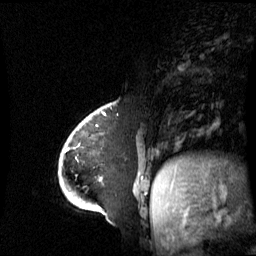
Breast MRI (dynamic contrast-enhanced), one sagittal slice; slice 17 of 60 in the series (ordered by position); dynamic contrast-enhanced series, image 2 of 3 at this slice position (ordered by acquisition); 1.5 T; TE 4.2 ms, TR 8.4 ms; 256 × 256 image matrix, field of view 270 × 270 mm. Female patient, age 43 years. Case-level facts recorded for this patient, not image findings: setting: breast cancer imaged before/during neoadjuvant chemotherapy; receptor status: triple-negative.
Annotated regions visible in this slice (semi-automatic segmentation, software-assisted and operator-edited):
- analysis volume of interest (the breast-tissue region the enhancement analysis was run in; not a lesion): box from (x=65, y=118) to (x=143, y=198) px
- tumour enhancement mask (voxels above the 70 % enhancement threshold inside the analysis volume of interest): (x=65, y=148)–(x=102, y=181)